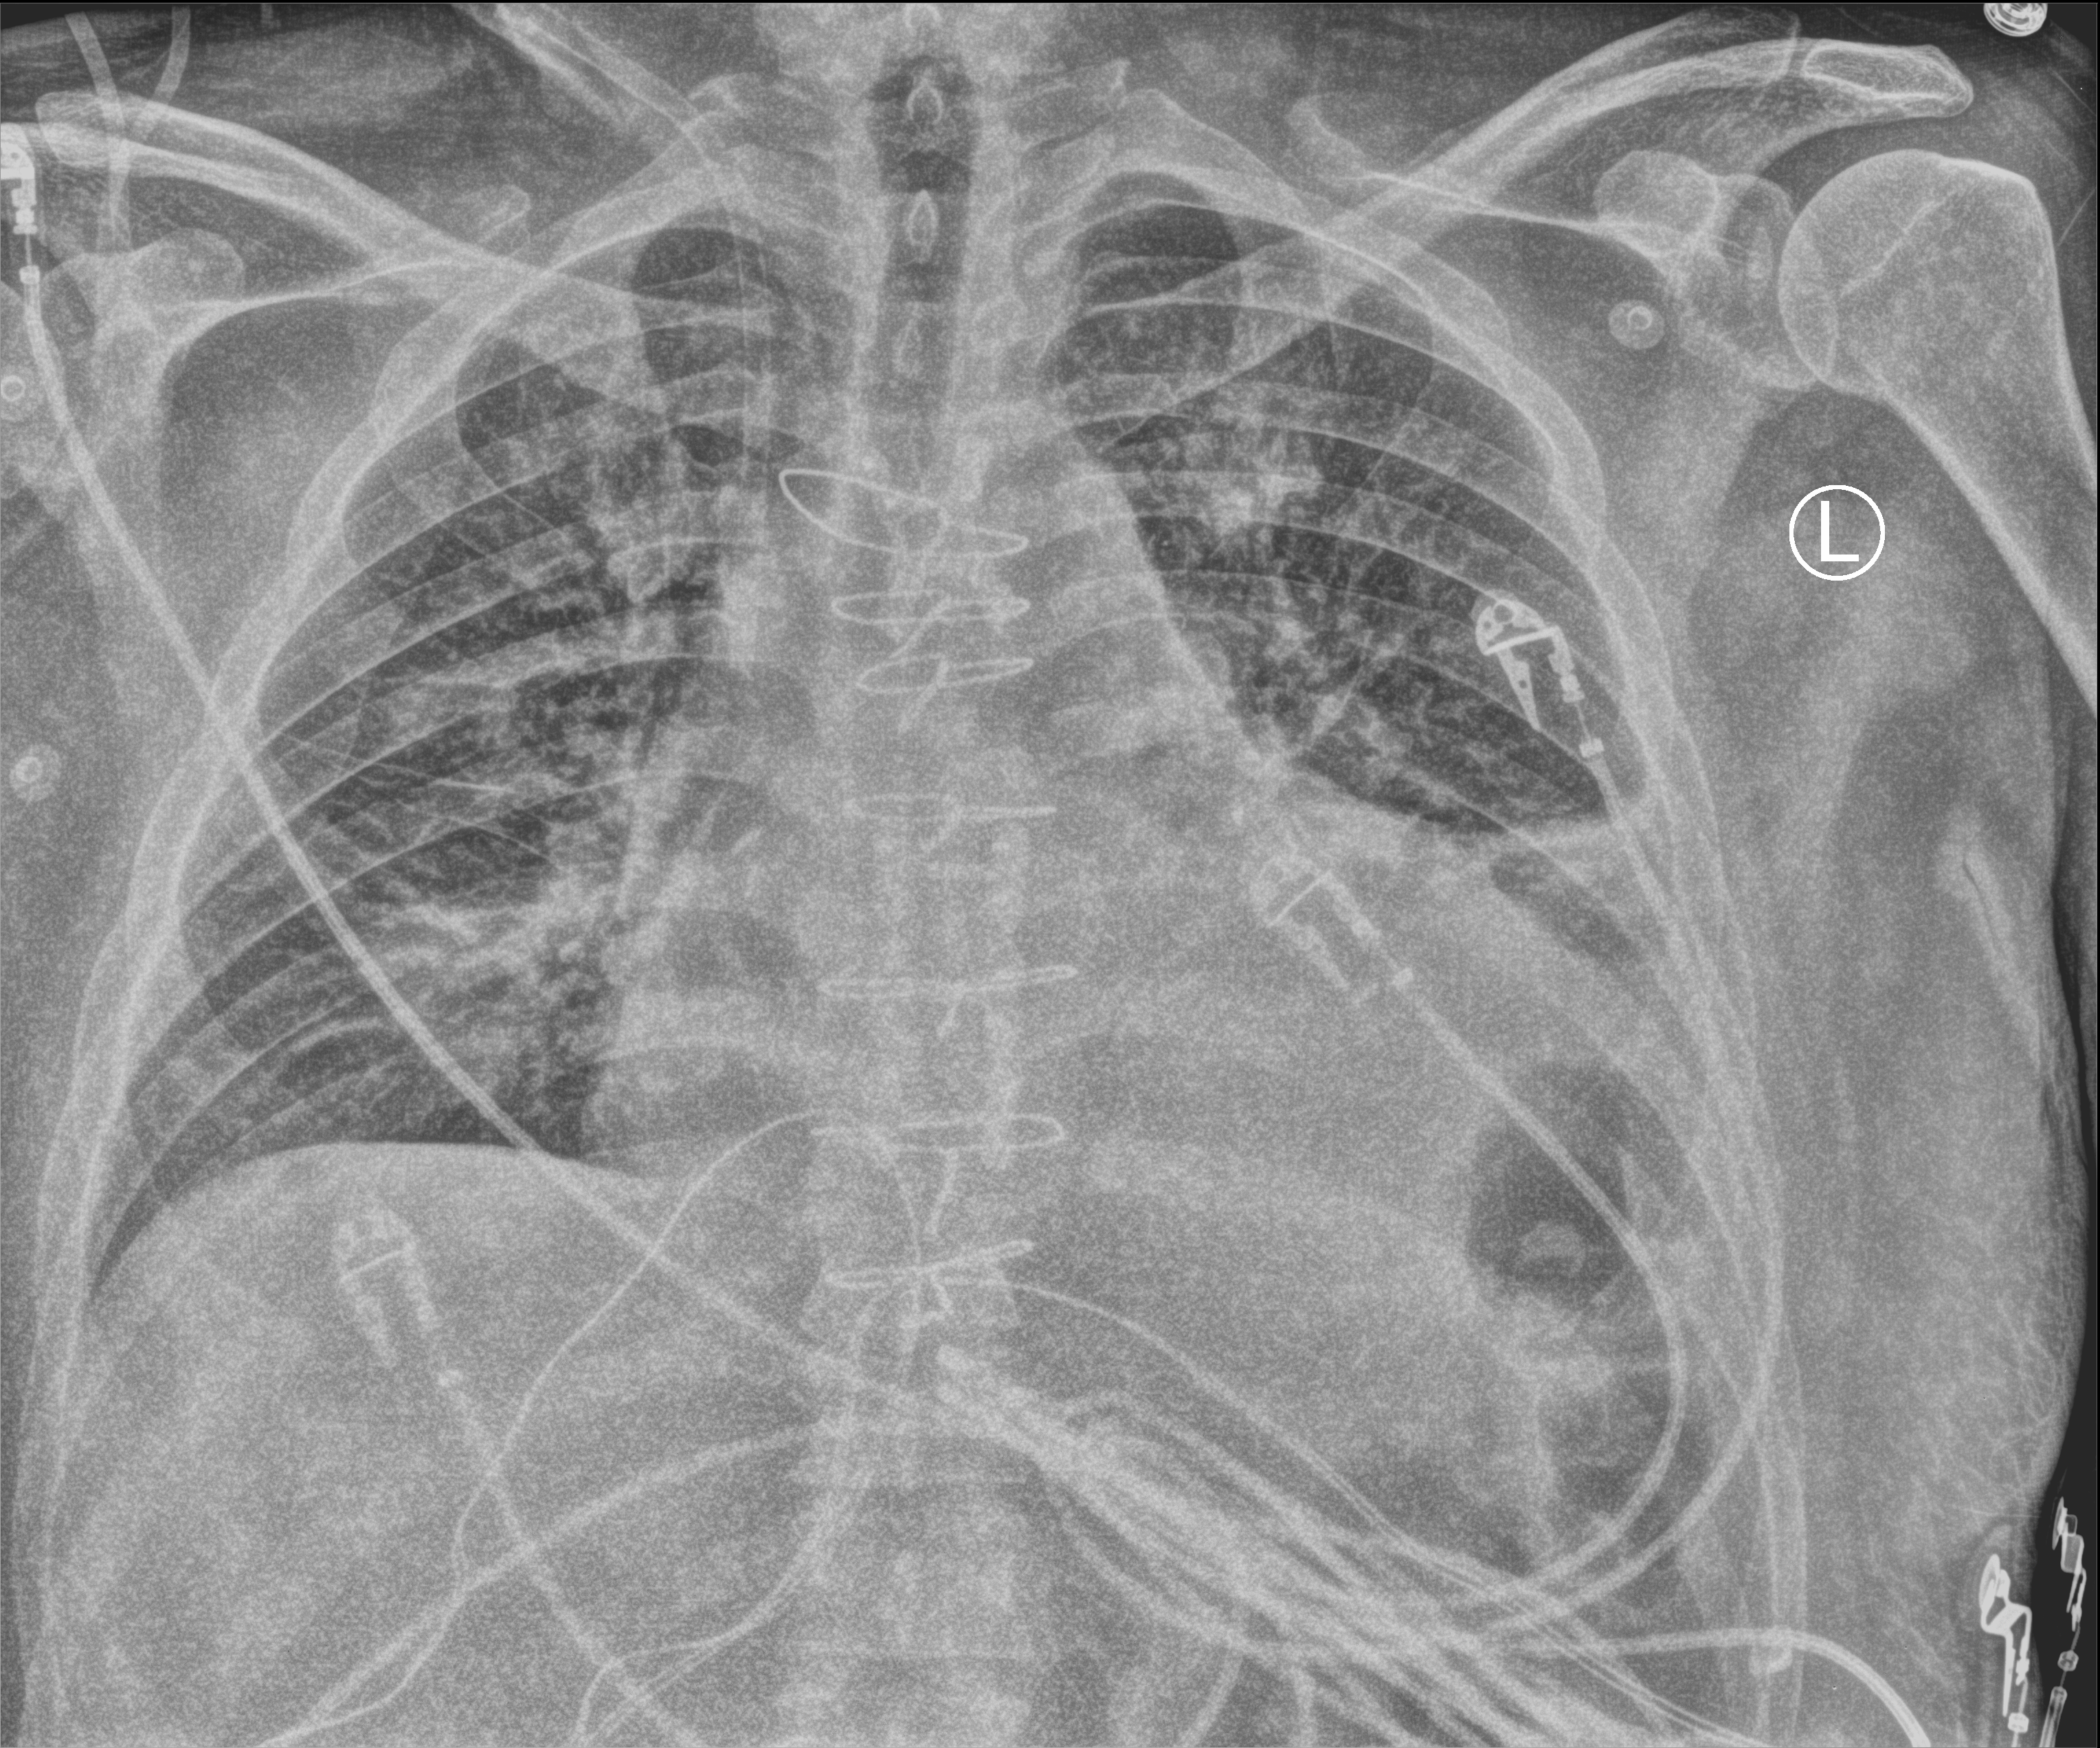
Chest X-ray (portable); anteroposterior (AP) projection. Patient hospitalised with COVID-19; male, aged 18–59 years.
Admission-level facts for this patient (not findings on this image; timing relative to this image not recorded): admitted to intensive care during this hospital stay: no; mechanically ventilated during this hospital stay: no.